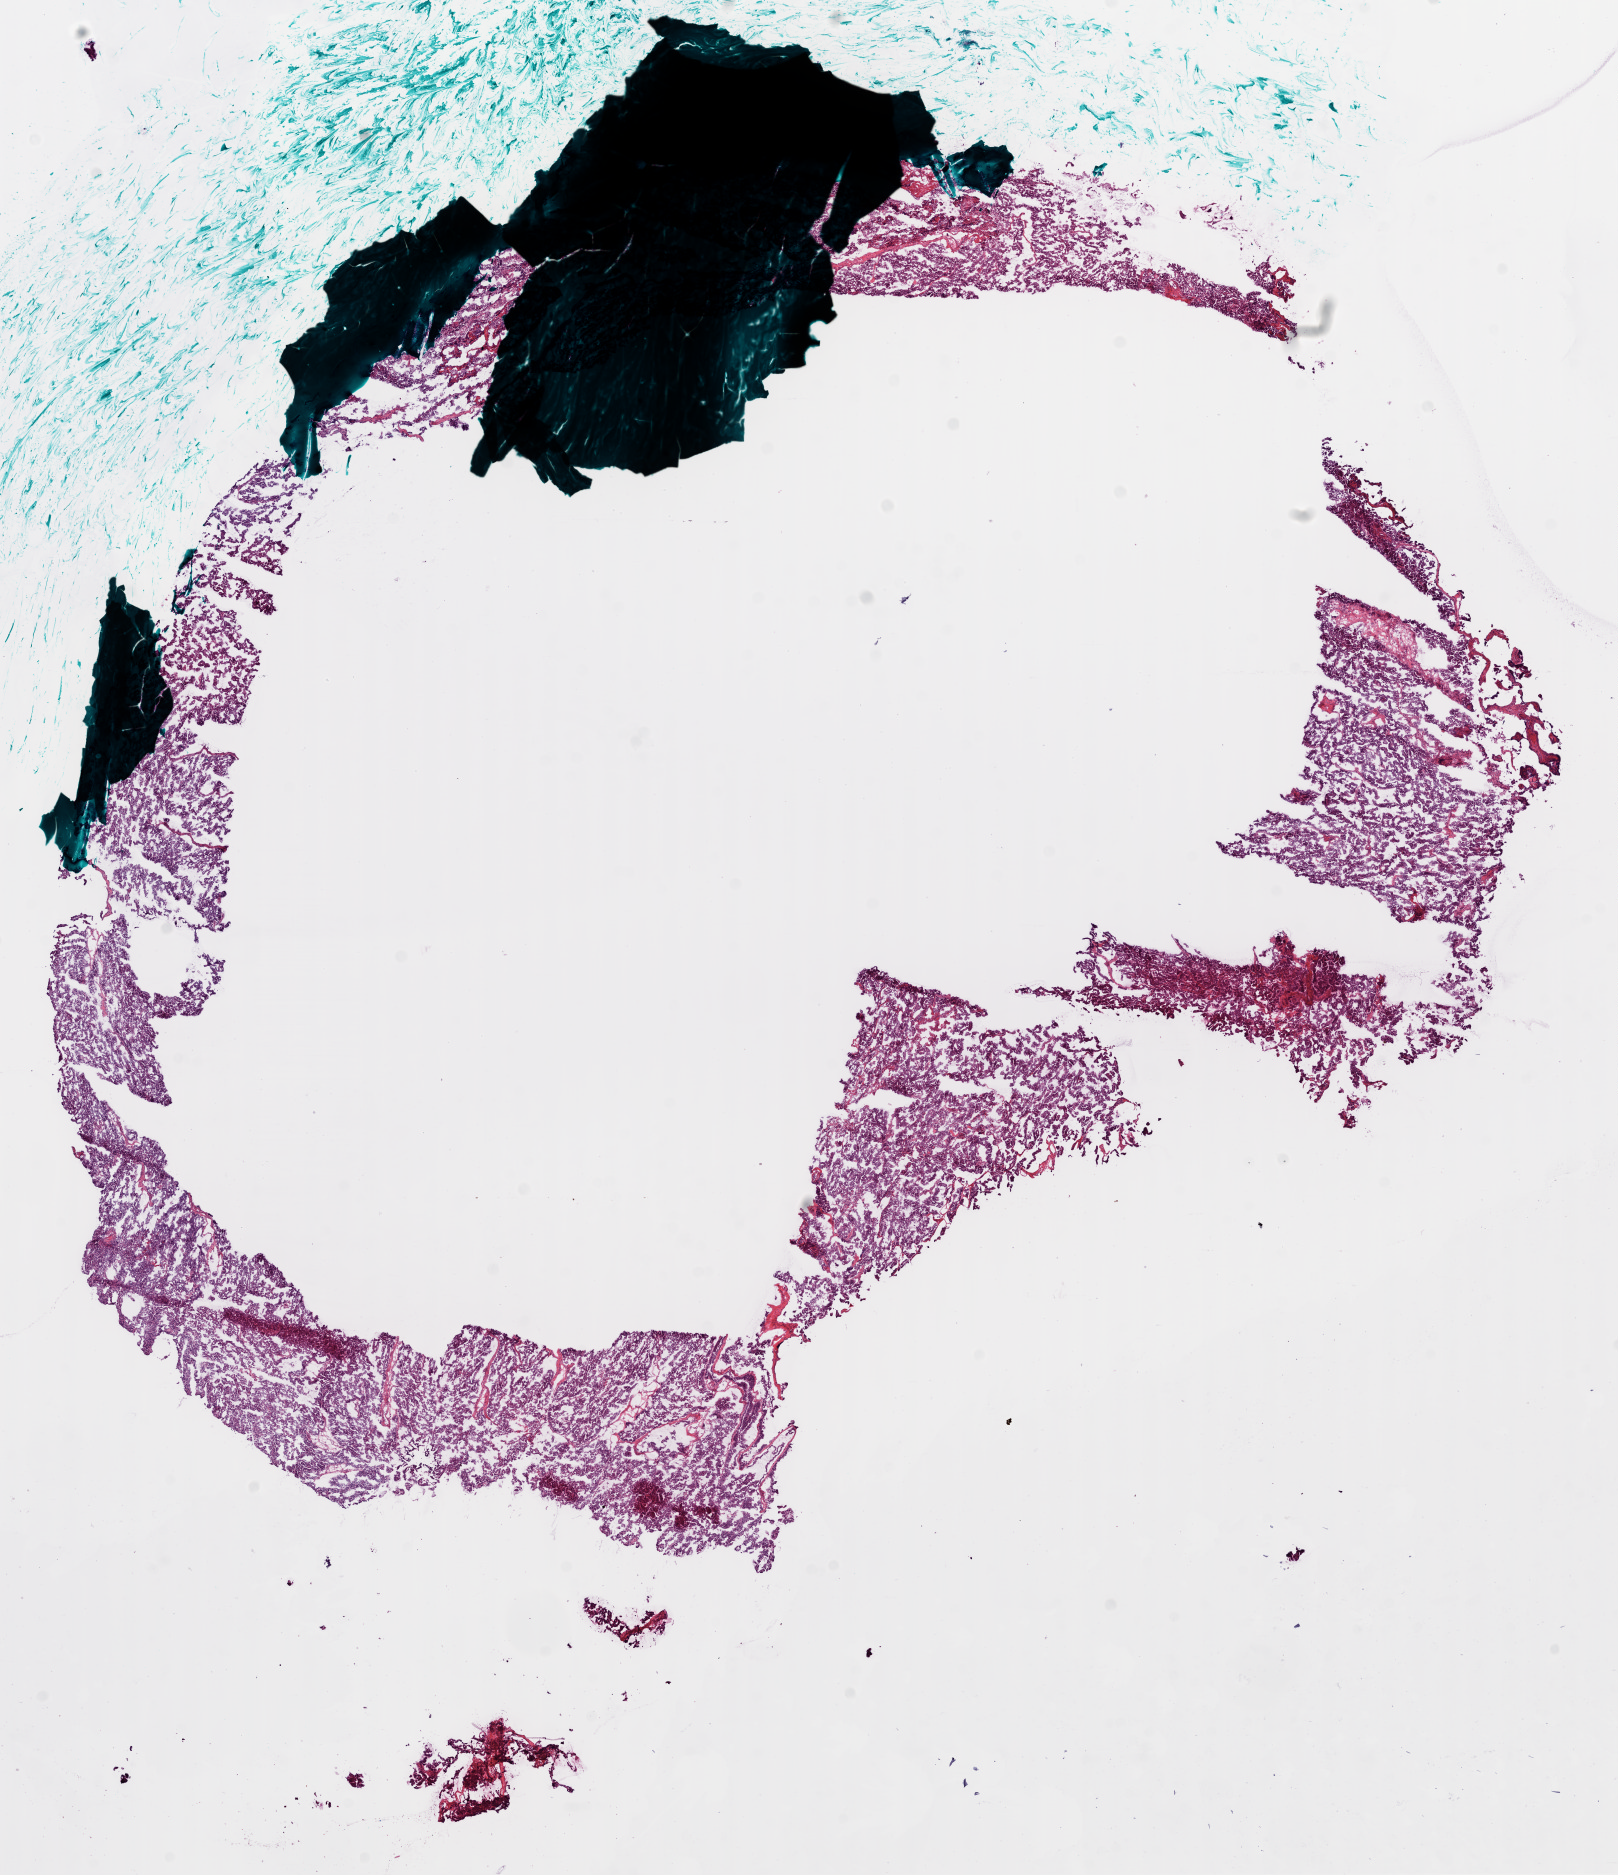
Digitized Hematoxylin and eosin (H&E) stained tissue section (whole slide), shown as a low-resolution overview of the whole scanned area (about 13.1 x 15.1 mm, acquisition: 20x scan). Frozen section from the bottom of the tissue portion. Sample: primary tumour, ovary. Female patient; age at initial diagnosis 44 years. Histologic grade: GX (grade cannot be assessed). Pathologist review of this section (percent, as recorded): tumour cells 94%, tumour nuclei 95%, normal cells 5%, necrosis 1%.
* pathologic diagnosis: Serous cystadenocarcinoma, NOS
* FIGO stage: IIIC
* laterality: bilateral